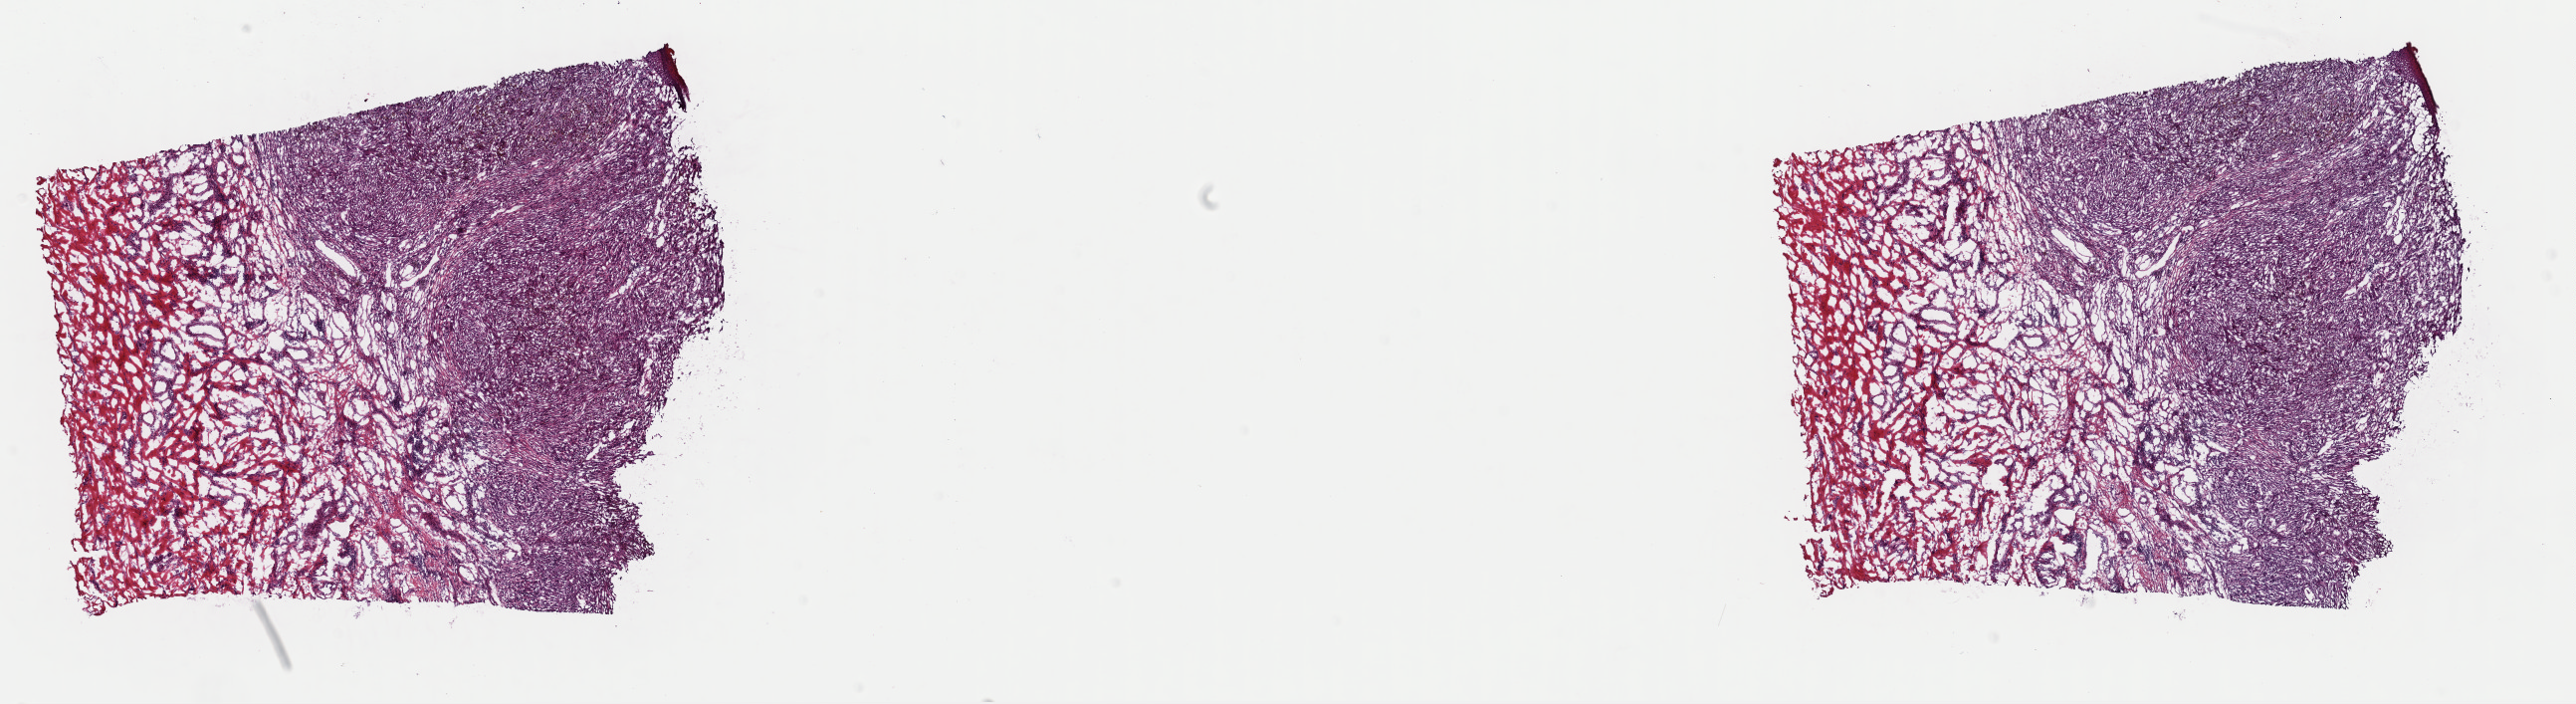
Whole-slide histology image, H&E — shown as a low-resolution overview of the whole scanned area (about 20.4 x 5.6 mm), frozen section from the top of the tissue portion, skin, primary tumour sample. Female, age 77 years at initial diagnosis. Composition of this section per pathologist review: tumour cells 80%, tumour nuclei 80%, normal cells 0%, stromal cells 20%, necrosis 0%. Infiltration values recorded for this section: lymphocyte infiltration 3%, monocyte infiltration 1%, neutrophil infiltration 1%.
- AJCC pathologic stage: IIA
- pathologic diagnosis: Malignant melanoma, NOS